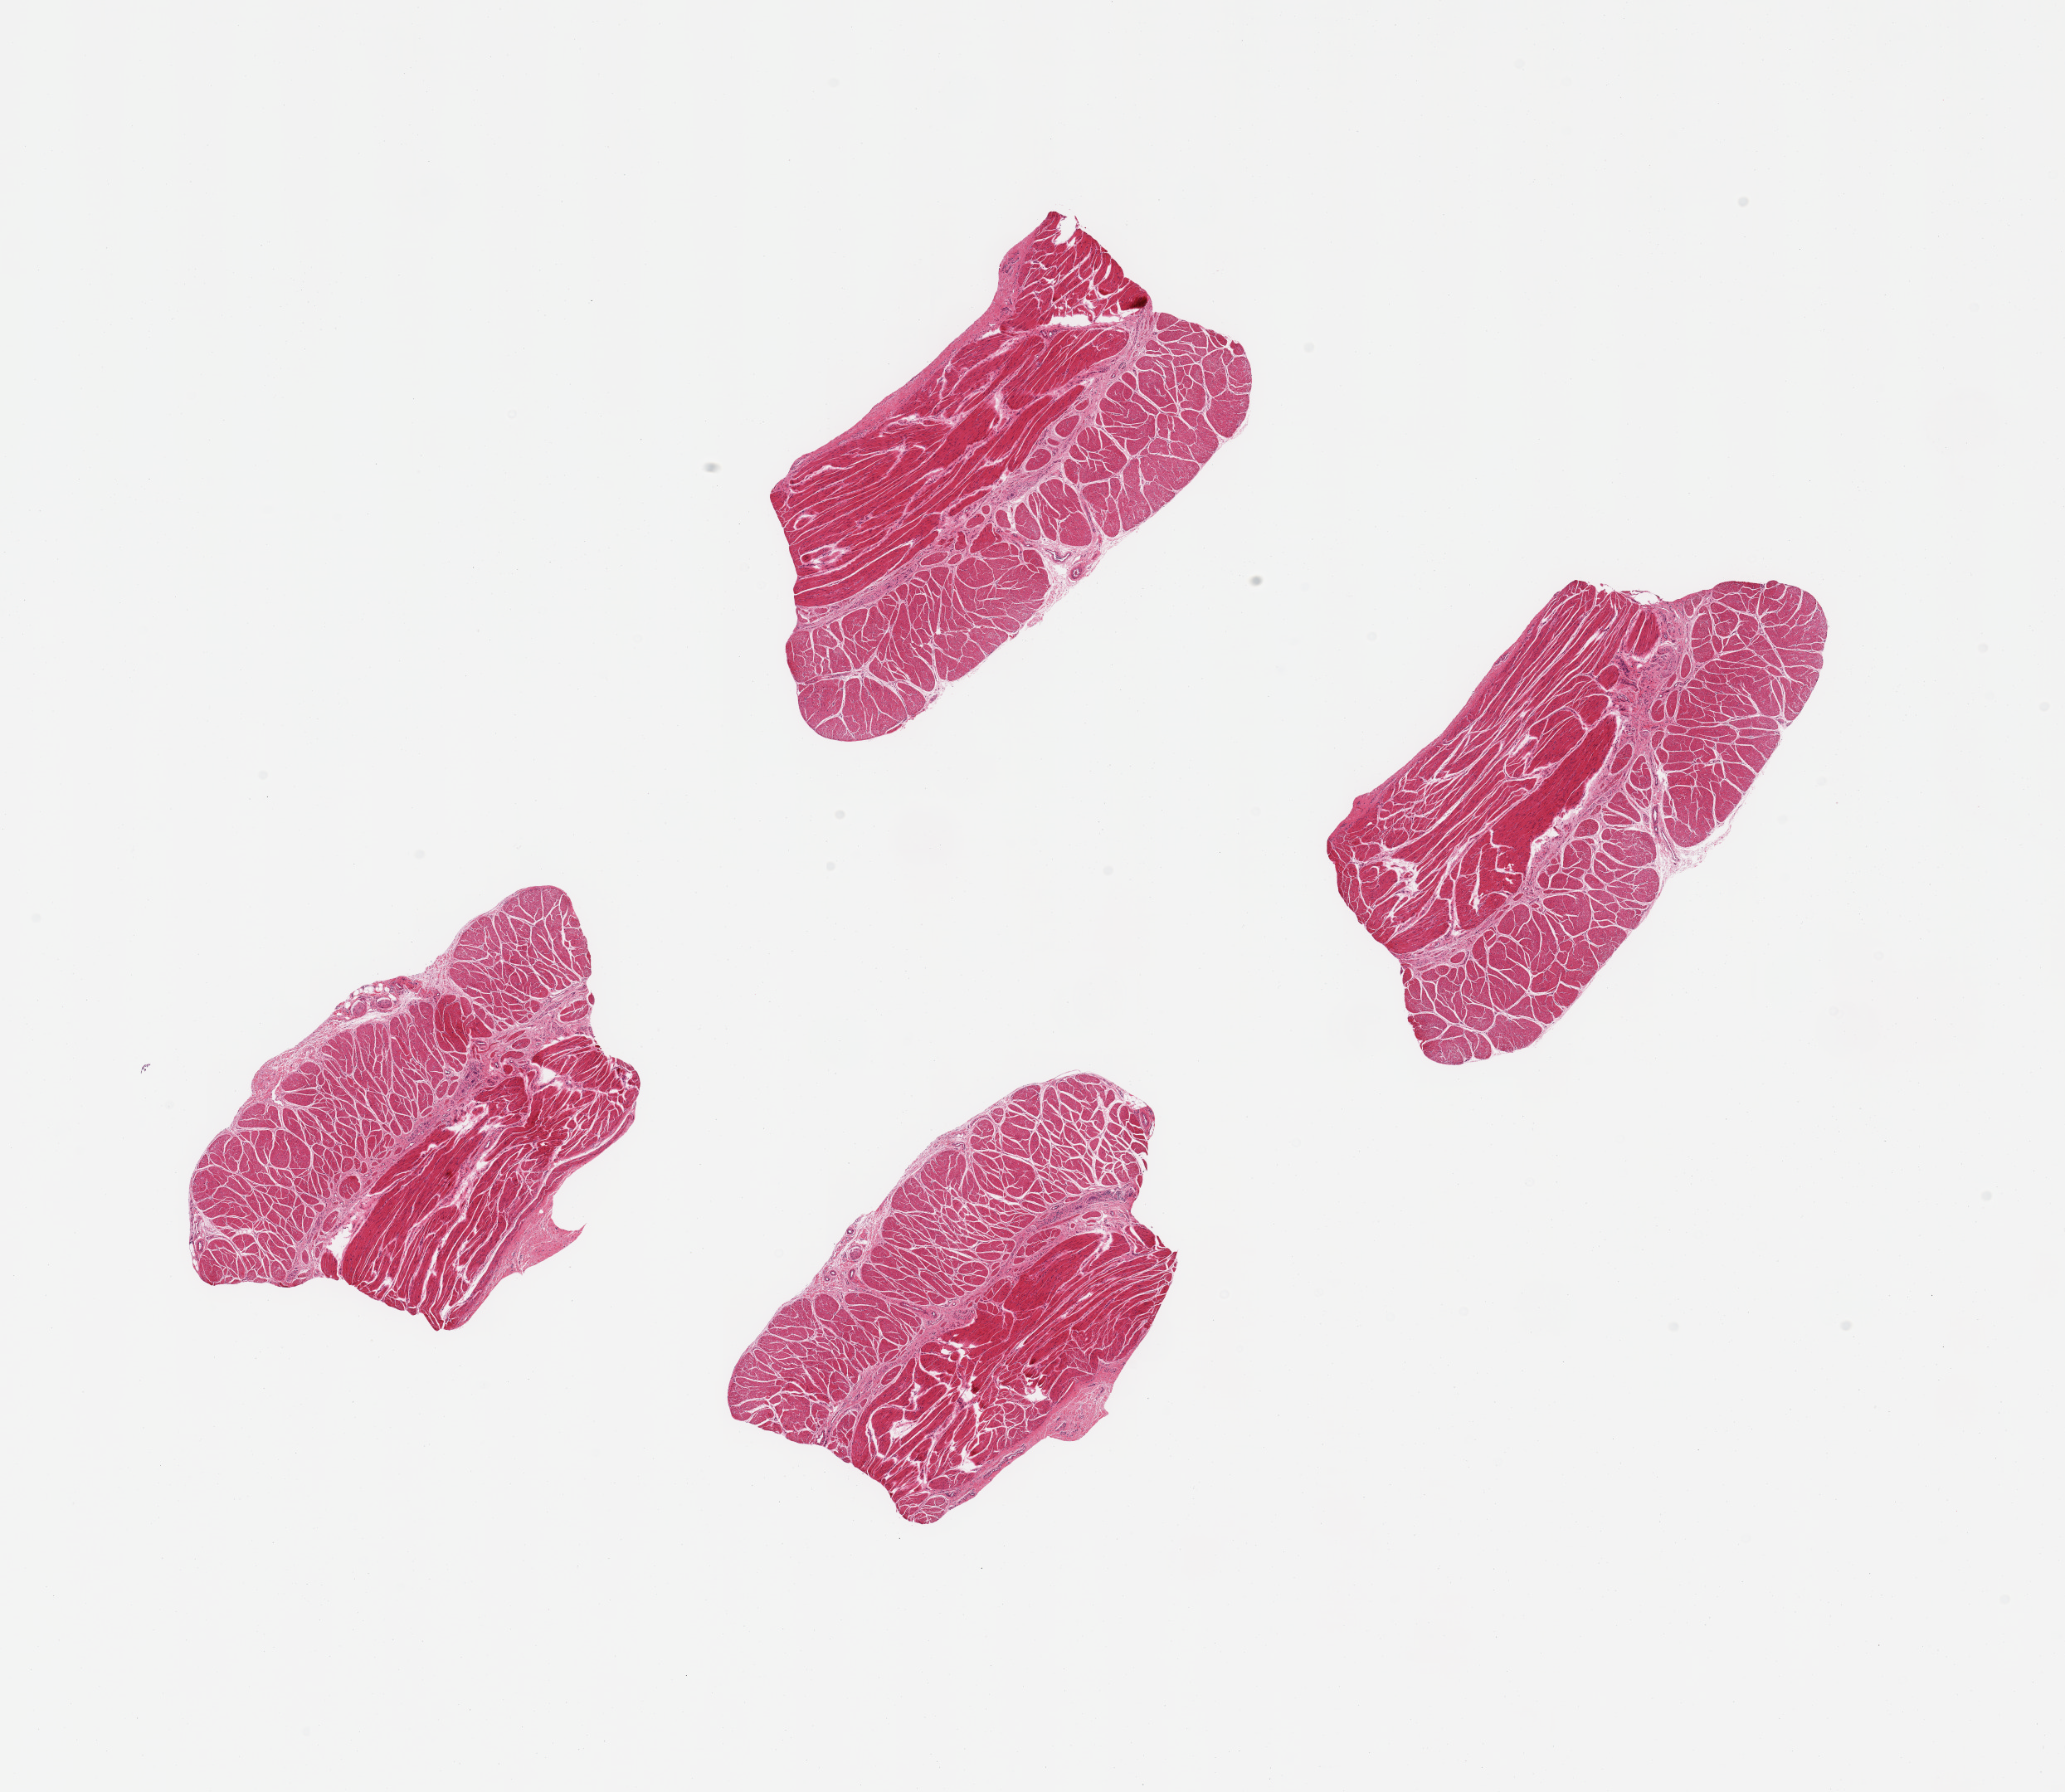
H&E whole-slide image, whole scanned area (about 19.7 x 17.1 mm) shown as a low-resolution overview; PAXgene-fixed, paraffin-embedded tissue; section of esophageal muscle (target tissue); tissue donor sample. Donor: male.
- reviewer comment on this tissue sample: 4 pieces; well dissected muscularis